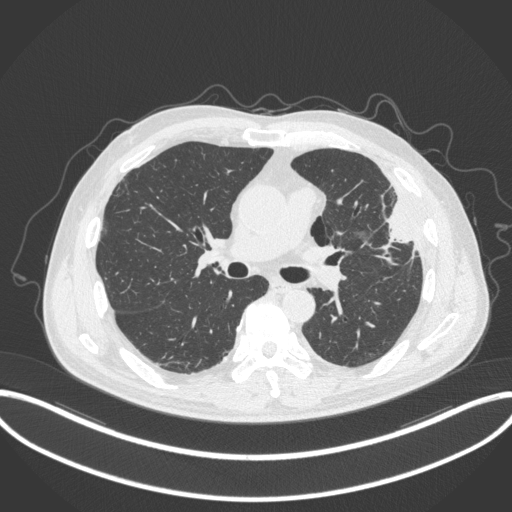
Chest CT, one axial slice; position 195 of 382 along the scan axis; reconstruction kernel B31f; lung window (W 1500 / L -600 HU); 1 mm slice thickness; 512 × 512 image matrix, field of view 415 × 415 mm. Patient: male, 64 years. From the clinical record (not read from this slice): clinical TNM (as recorded): T4 N1 M0; histopathological grade: G3.
Annotated regions visible in this slice (rectangle marked by the reading radiologist):
- lung tumour (recorded histology: adenocarcinoma): bounding box (x1, y1, x2, y2) in pixels: (380, 196, 417, 257)